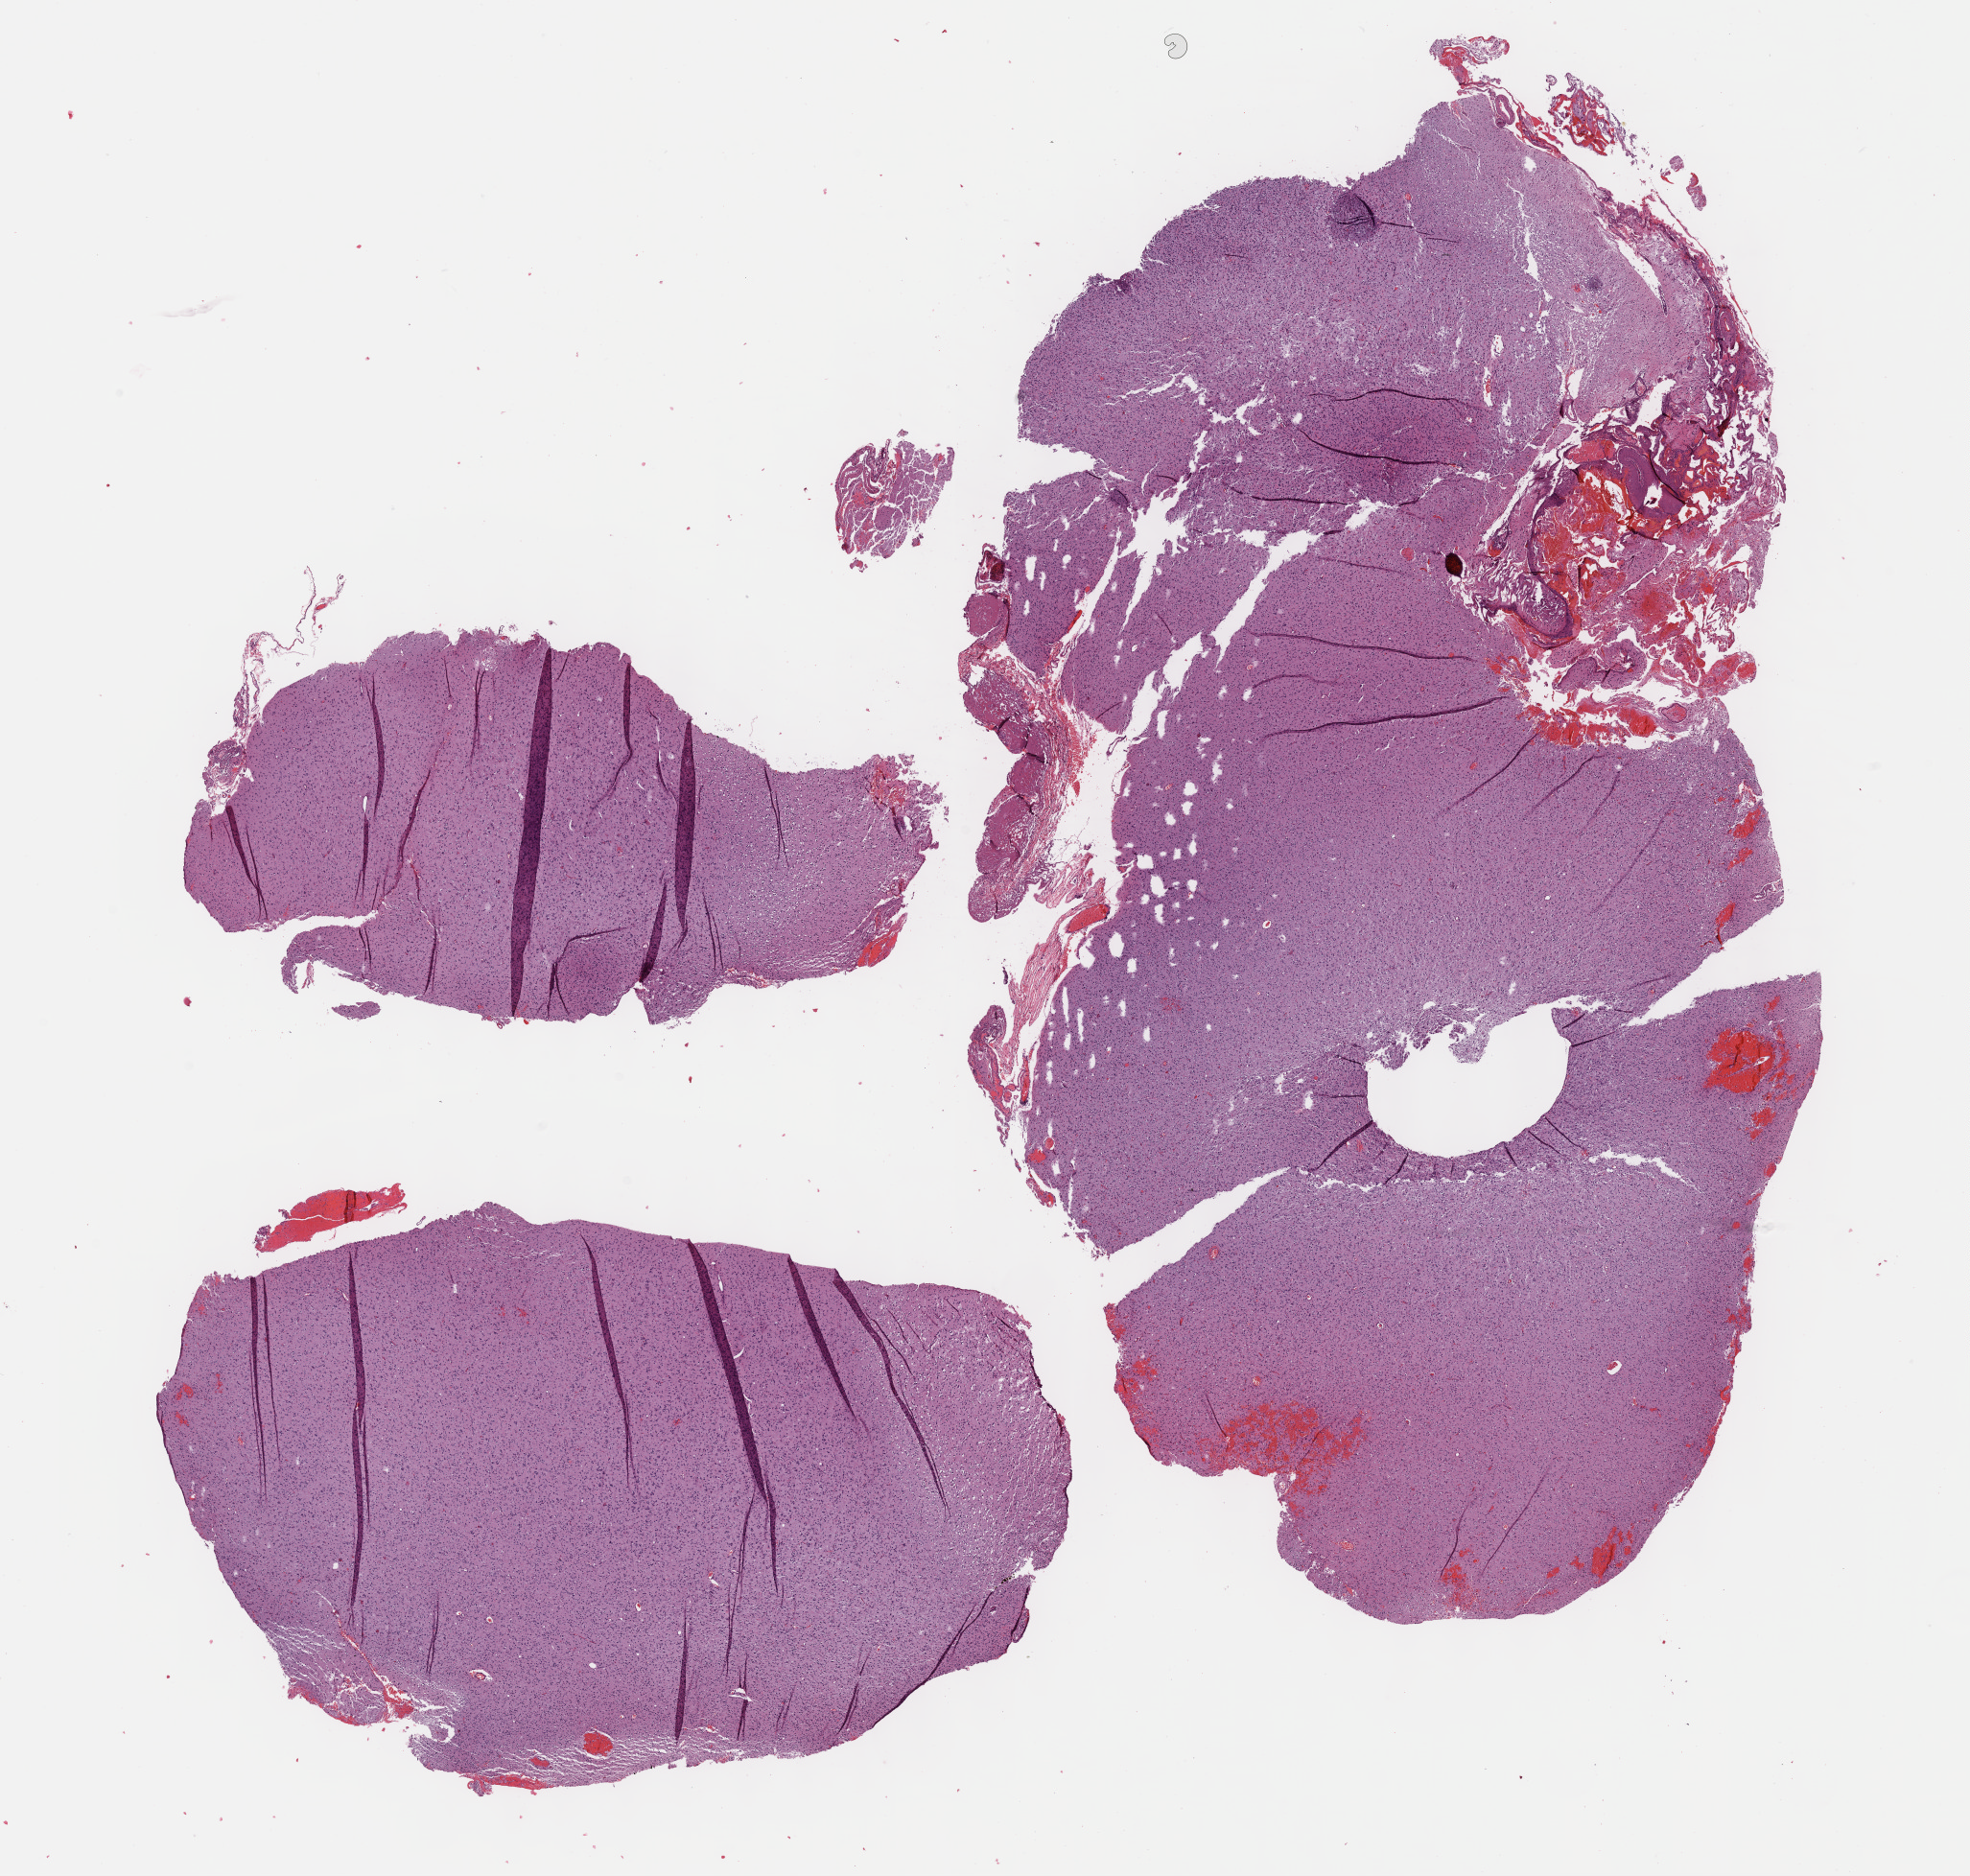
Digitized H&E tissue section (whole slide) — shown as a low-resolution overview of the whole scanned area (about 16.6 x 15.8 mm). FFPE section. Sample: primary tumour, brain. Male patient; age at initial diagnosis 52 years. Histologic grade: G2 (moderately differentiated).
Pathologic diagnosis: Mixed glioma (cerebrum).